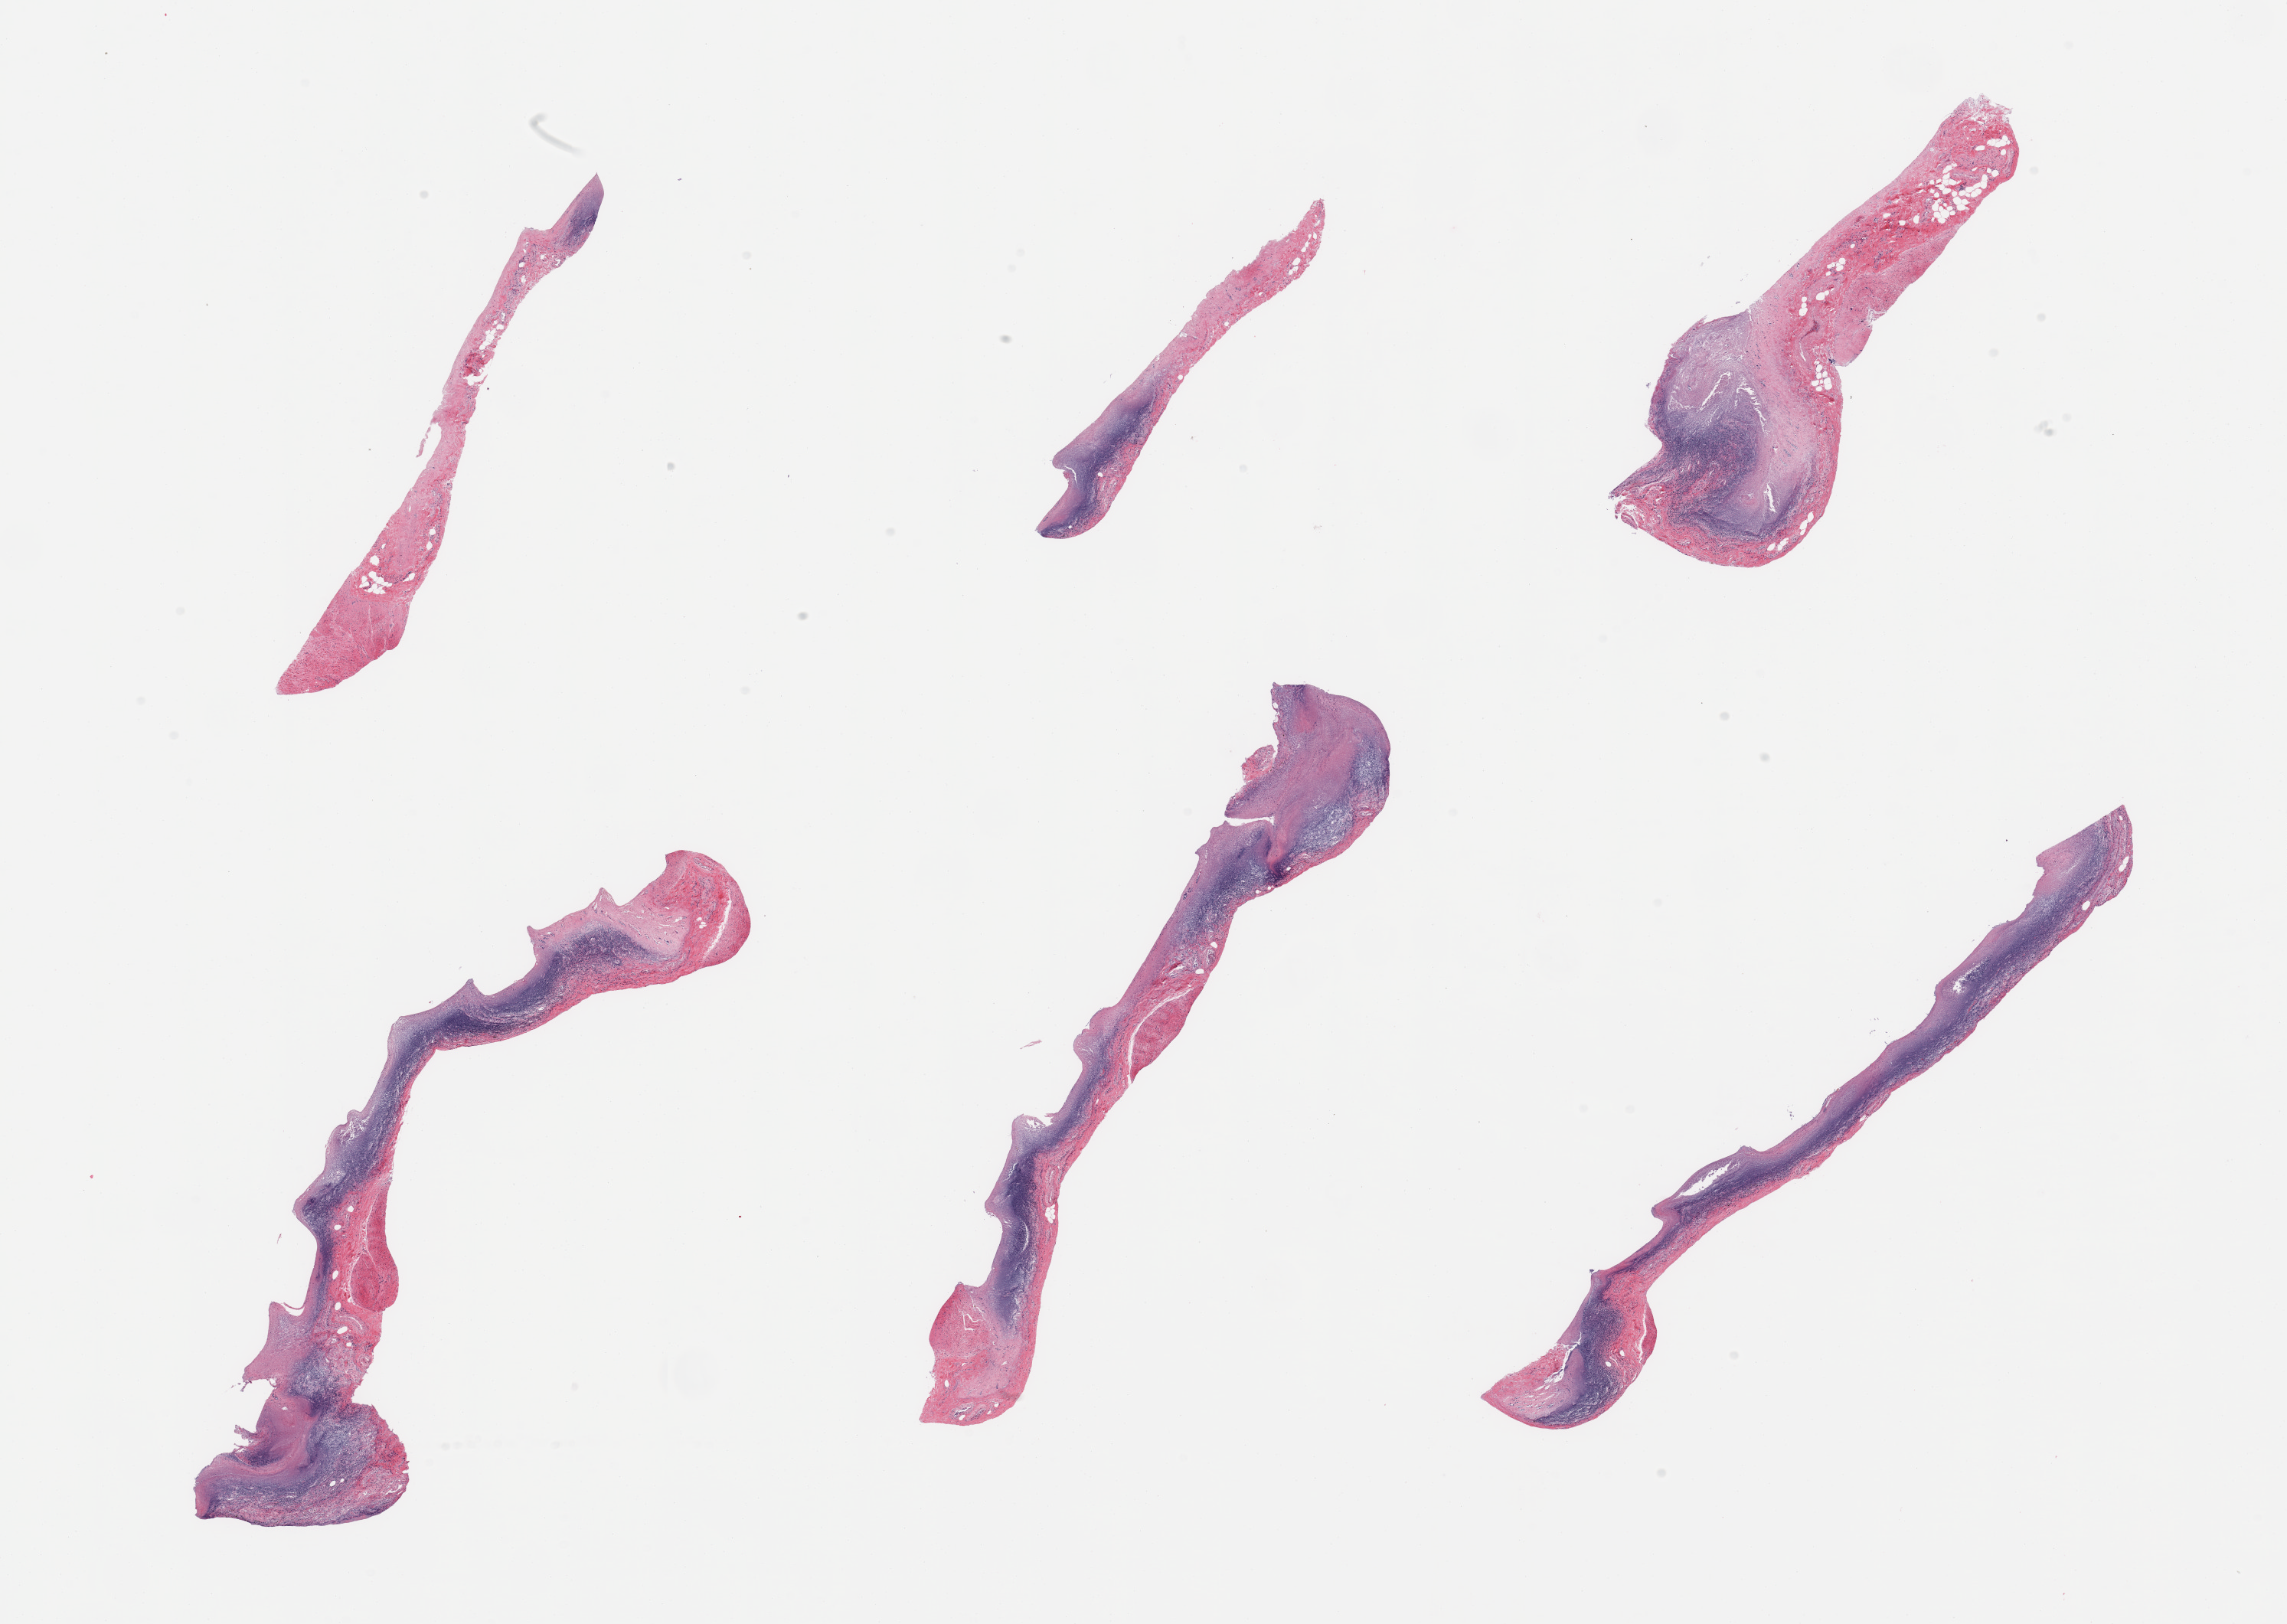
Digitized hematoxylin and eosin (H&E)-stained section — a low-resolution overview of the entire scanned area, about 23.6 x 16.8 mm (from a 20x scan); PAXgene-fixed paraffin-embedded (PFPE) section; target tissue: ileum; tissue donor sample.
• reviewer comment on this tissue sample: 6 pieces; totally autolyzed mucosa and abundance of moderately autolyzed mucosal lymphoid tissue; focally muscularis present, not target